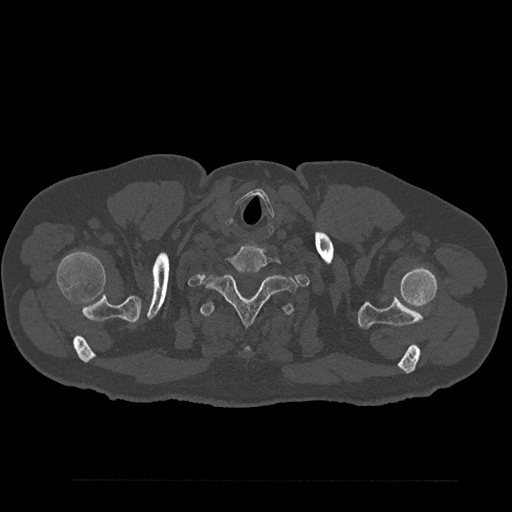
CT including the spine, one axial slice; position 753 of 797 along the scan axis; reconstruction kernel Br40s/3; 120 kVp; bone window (W 1800 / L 400 HU); 512 × 512 image matrix, field of view 430 × 430 mm. Patient: male, 61 years. From the clinical record (not read from this slice): primary cancer: prostate.
Annotated regions visible in this slice (semi-automatic segmentation, software-assisted and operator-edited):
- T1 vertebra: box from (x=204, y=273) to (x=297, y=325) px
- T2 vertebra: (x=200, y=301)–(x=295, y=353)